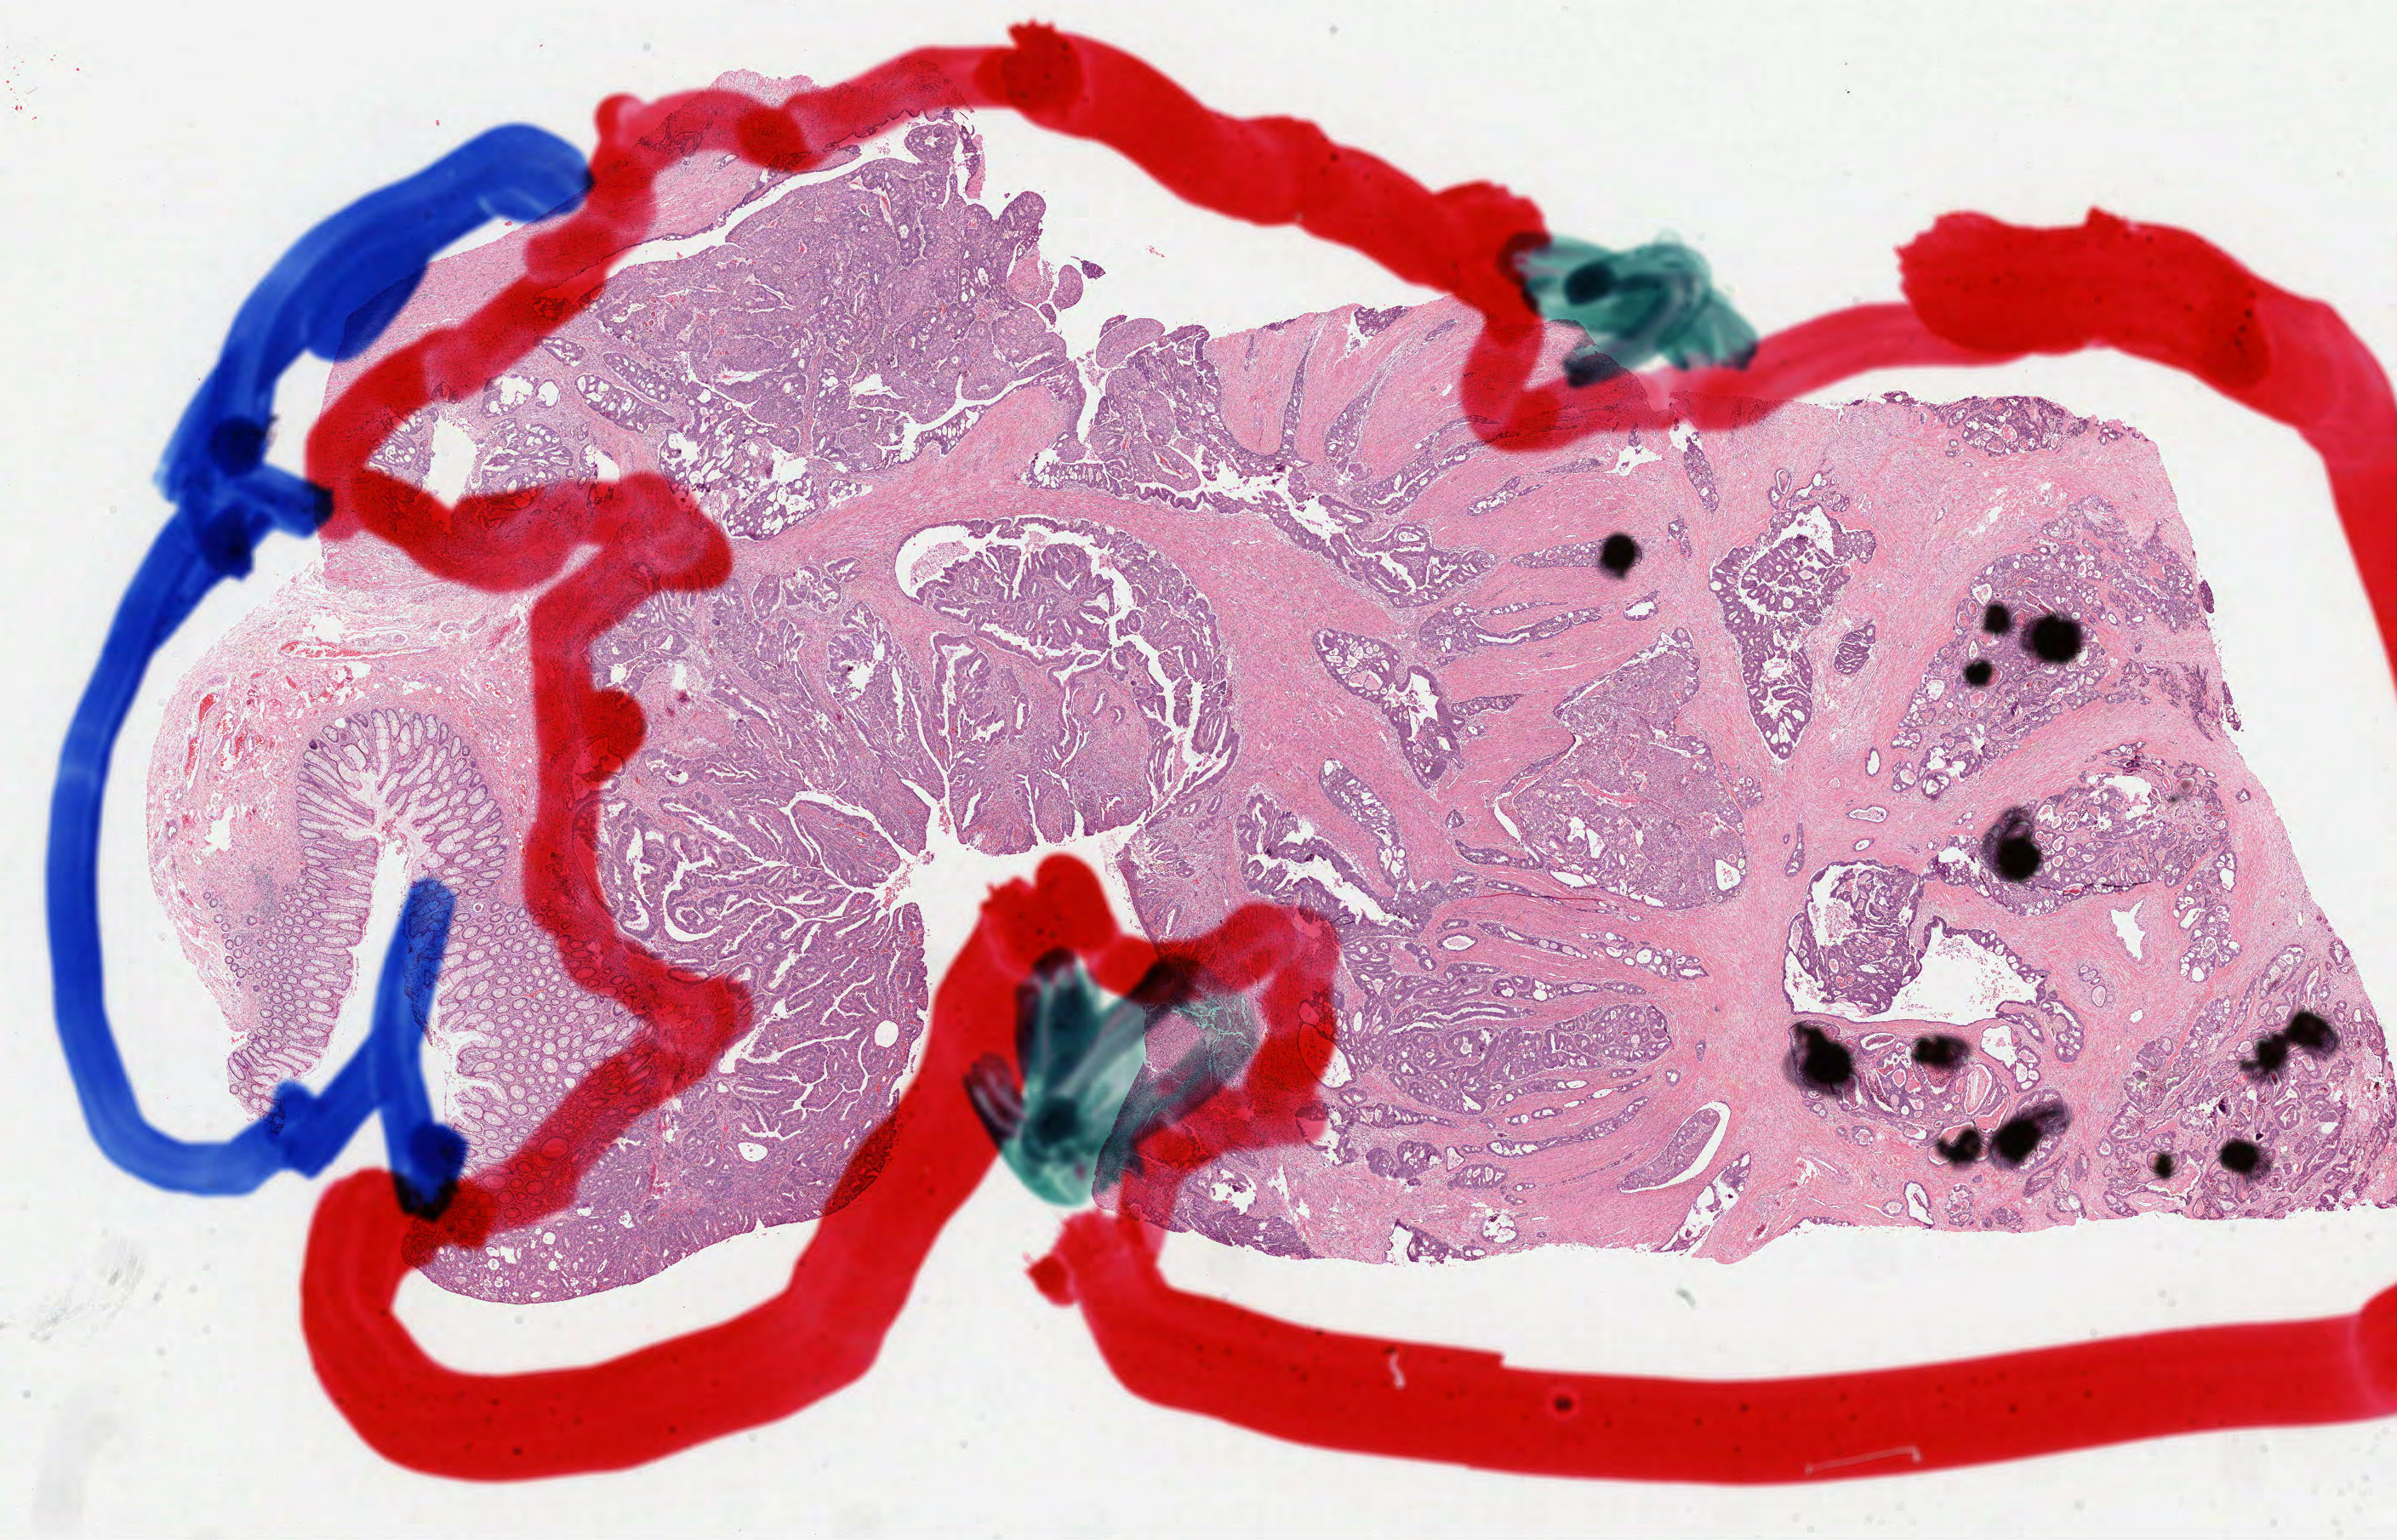
Digitized H&E-stained tissue section (whole slide) — low-resolution overview of the scanned area, about 22.7 x 14.6 mm, formalin-fixed paraffin-embedded (FFPE) diagnostic section, primary tumour sample from the rectum. Female patient; age at initial diagnosis 71 years.
AJCC pathologic stage: IIIB. Lymph nodes positive (case pathology): 3 of 6 examined. Diagnosis: Adenocarcinoma, NOS.